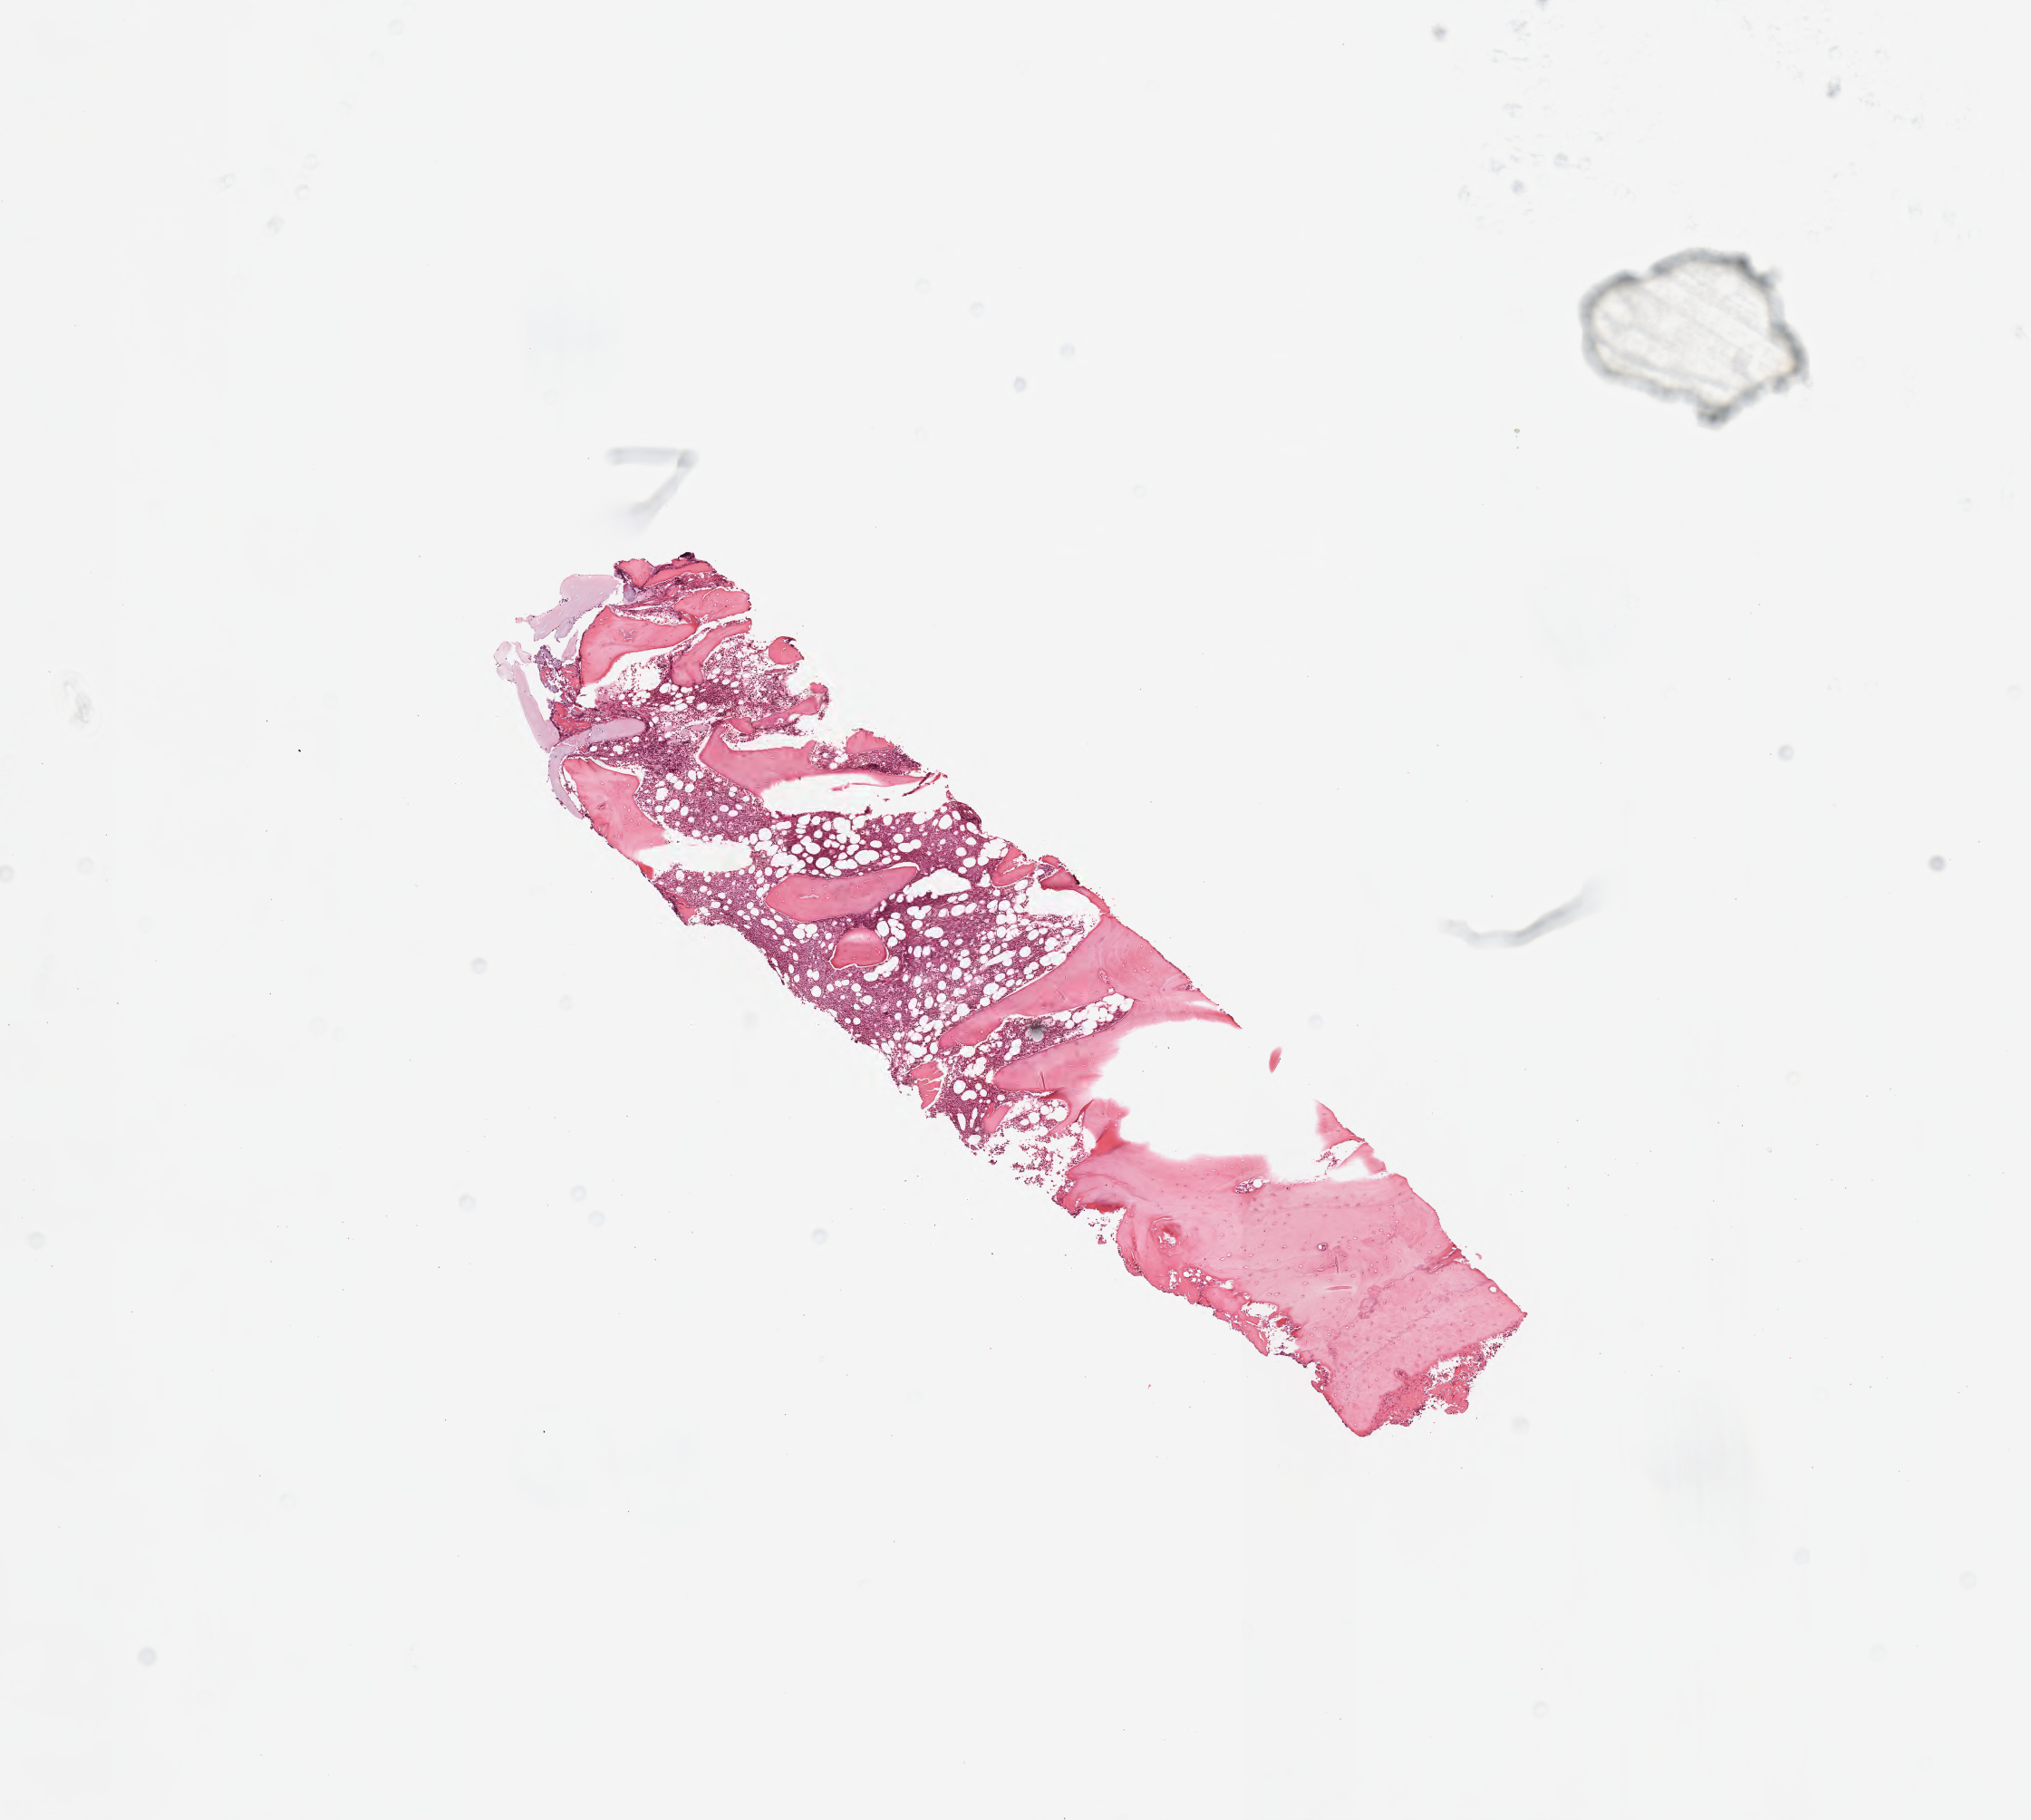
Haematoxylin and eosin whole-slide image — a low-resolution overview of the entire scanned area, about 9.1 x 8.1 mm; tumor tissue; site: bone marrow. Female, age 4 years at initial diagnosis.
* histologic diagnosis: Burkitt lymphoma, NOS